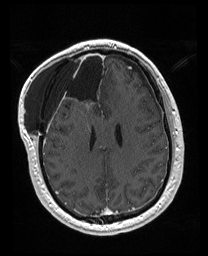
Brain MRI from a brain-tumour surgery series, one axial slice; position 68 of 176 along the scan axis; T1-weighted post-contrast; 208 × 256 image matrix, field of view 208 × 256 mm. From the clinical record (not read from this slice): histopathology: Astrocytoma; WHO grade: 4.
Annotated regions visible in this slice (expert manual segmentation):
- previous resection cavity: bounding box (x1, y1, x2, y2) in pixels: (59, 52, 102, 111)